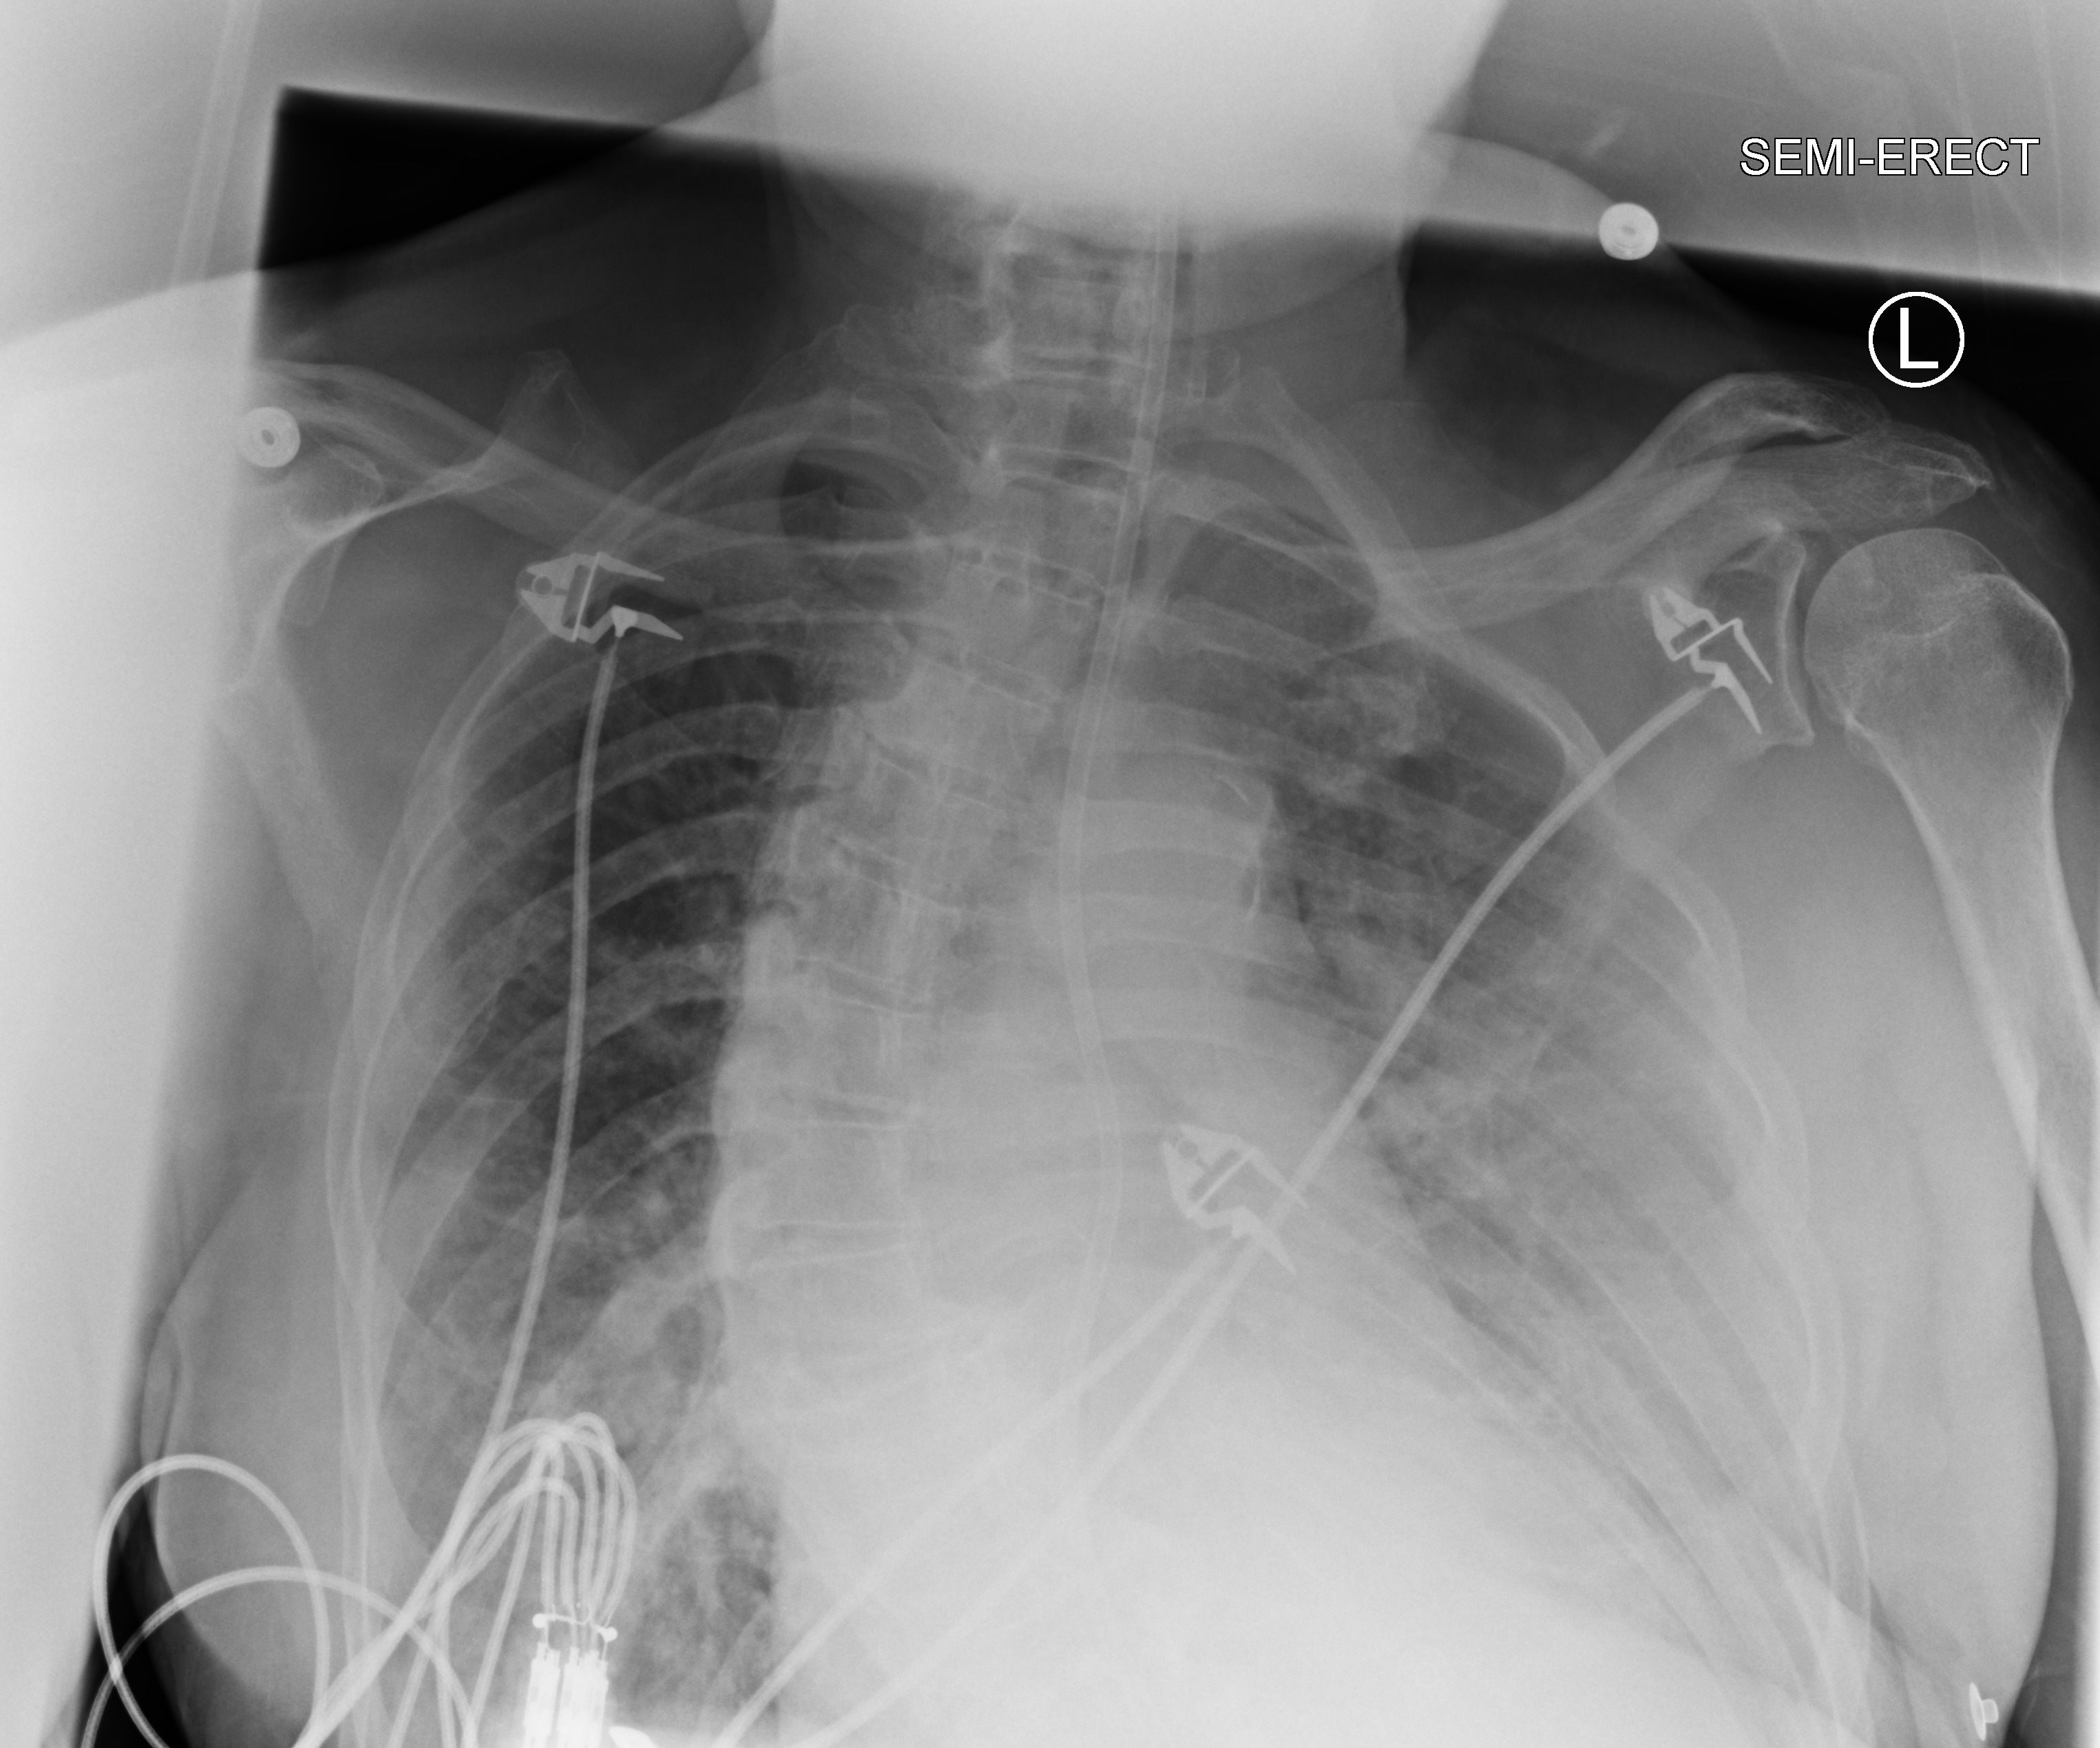
Portable chest radiograph; anteroposterior (AP) projection. Male patient hospitalised with COVID-19, age 75–90 years.
Hospital-stay facts (about this admission, not read from this image; timing relative to this image not recorded):
- admitted to intensive care during this hospital stay: no